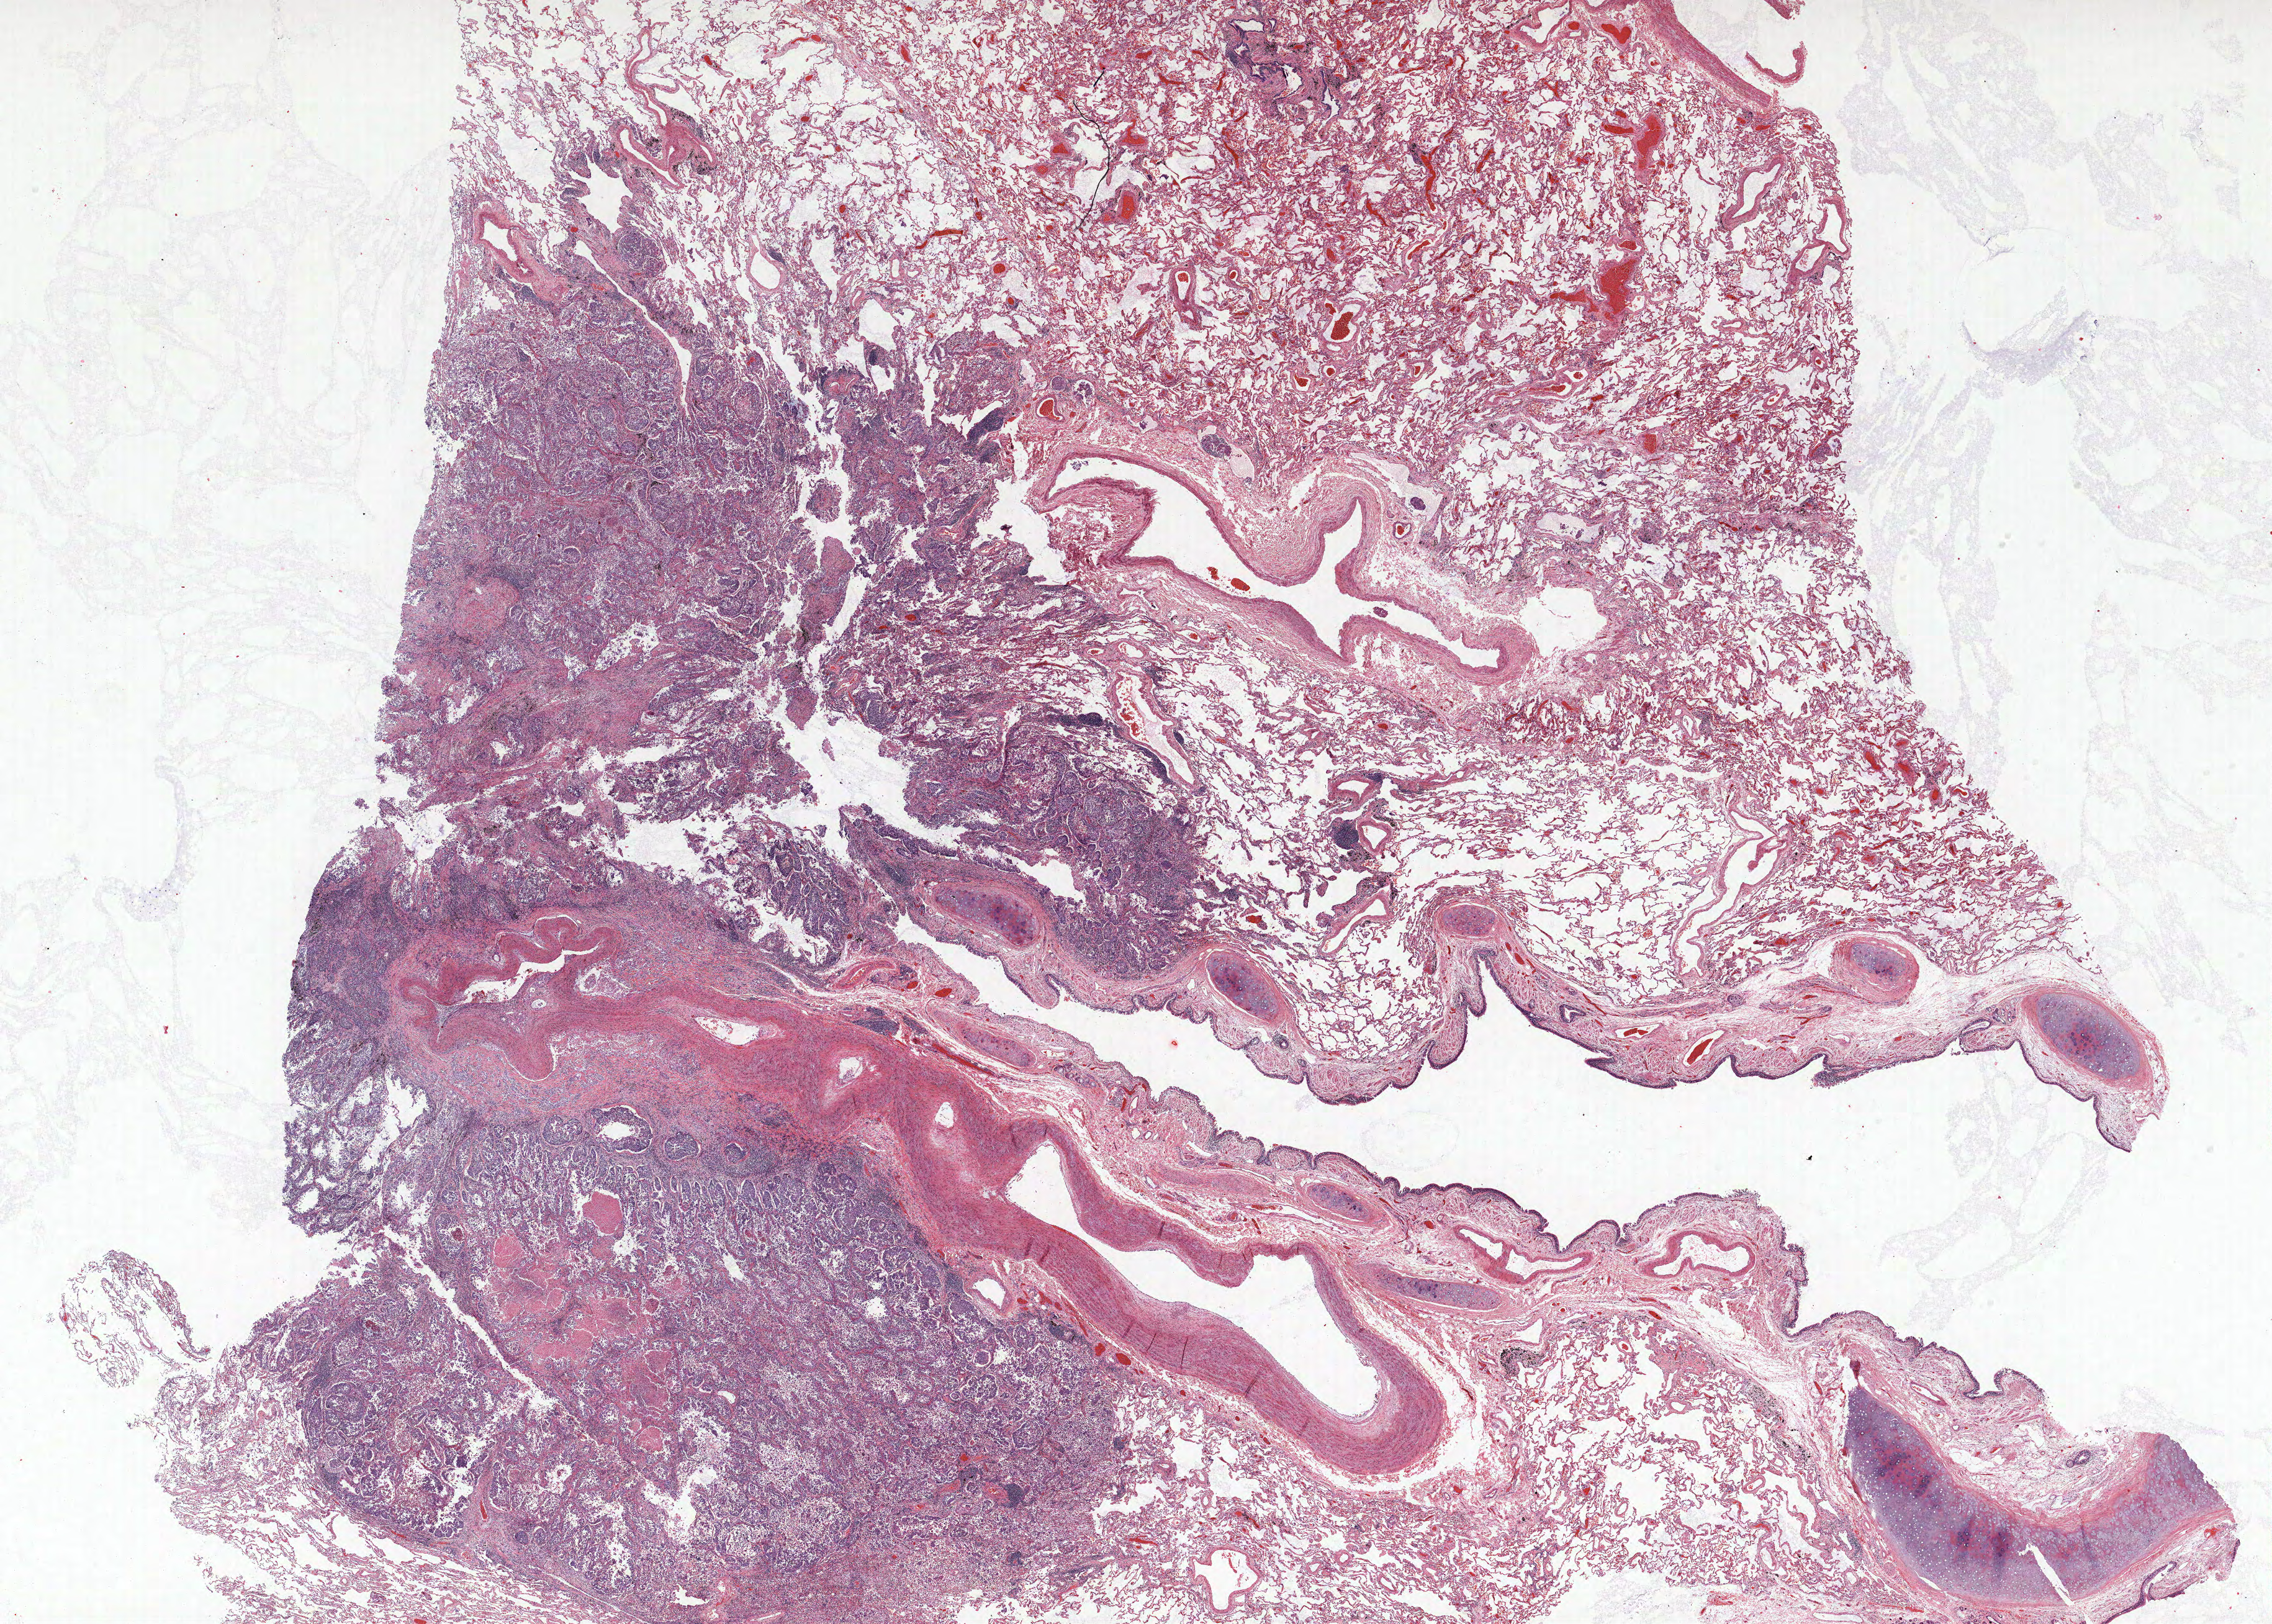
Hematoxylin and eosin (H&E) stained whole-slide image — whole scanned area (about 29.3 x 20.9 mm) shown as a low-resolution overview; FFPE section; lung tissue. Male, age 74 at enrolment. Grade: poorly differentiated (G3).
Stage (AJCC 6th edition): IIIA. Tumour size (pathology): 27 mm. Participant's lung-cancer diagnosis: Adenocarcinoma, NOS (ICD-O-3 8140/3). Primary tumour location (clinical record): left upper lobe.